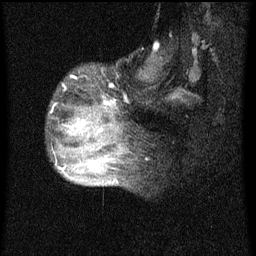
Breast MRI (dynamic contrast-enhanced), one sagittal slice; position 18 of 60 along the scan axis; dynamic contrast-enhanced series, image 2 of 4 at this slice position (ordered by acquisition); 1.5 T; TE 4.2 ms, TR 8 ms; 256 × 256 image matrix, field of view 180 × 180 mm. Patient: female, 50 years.
Annotated regions visible in this slice (semi-automatically segmented with operator editing):
- analysis volume of interest (the breast-tissue region the enhancement analysis was run in; not a lesion): bounding box <53,94,124,177> (left, top, right, bottom; pixels)
- tumour enhancement mask (voxels above the 70 % enhancement threshold inside the analysis volume of interest): <59,102,111,171>